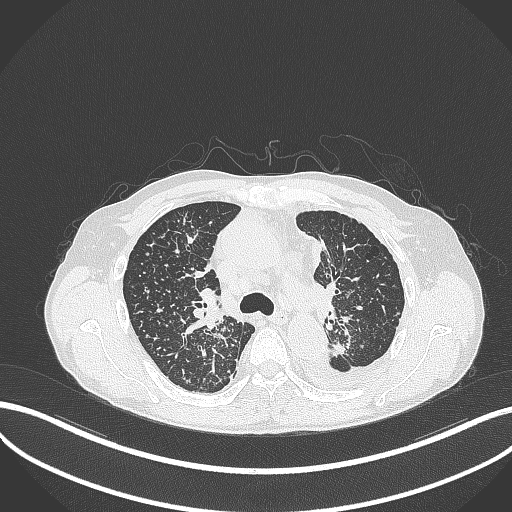
Chest CT, one axial slice; position 244 of 325 along the scan axis; lung window (W 1500 / L -600 HU); 512 × 512 image matrix. Patient: male, 58 years. Case-level facts recorded for this patient, not image findings: clinical TNM (as recorded): T1c N3 M1.
Outlined on this slice (rectangle marked by the reading radiologist):
- lung tumour (recorded histology: adenocarcinoma): bounding box <333,339,347,358> (left, top, right, bottom; pixels)